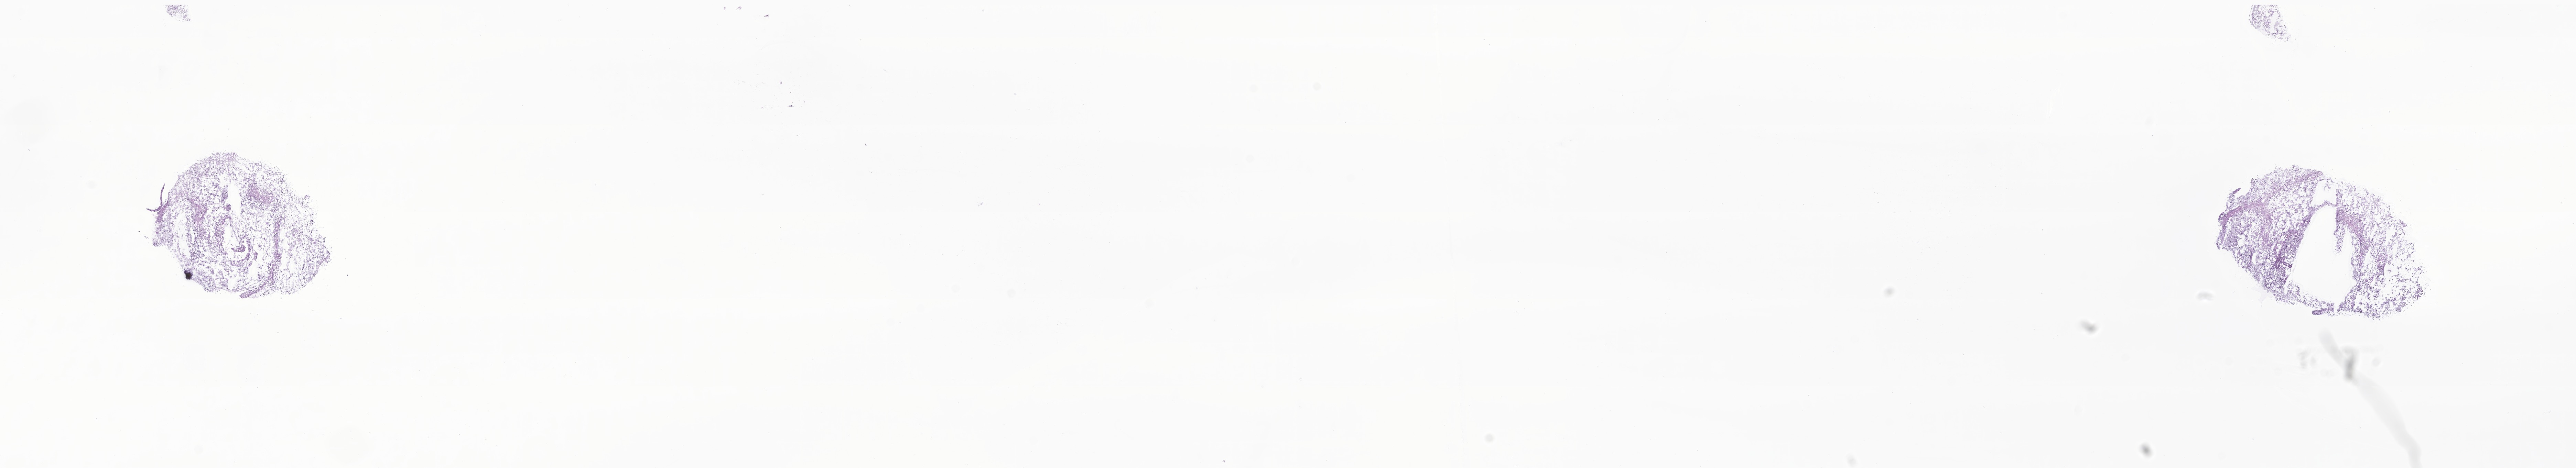
Digitized hematoxylin and eosin (H&E)-stained section of tumor tissue from the cerebellum — shown as a low-resolution overview of the whole scanned area (about 31.6 x 5.7 mm), cryosection (OCT / tissue freezing medium). Female patient, age 145 months.
• diagnosis (ICD-O-3 morphology term): Pilocytic astrocytoma